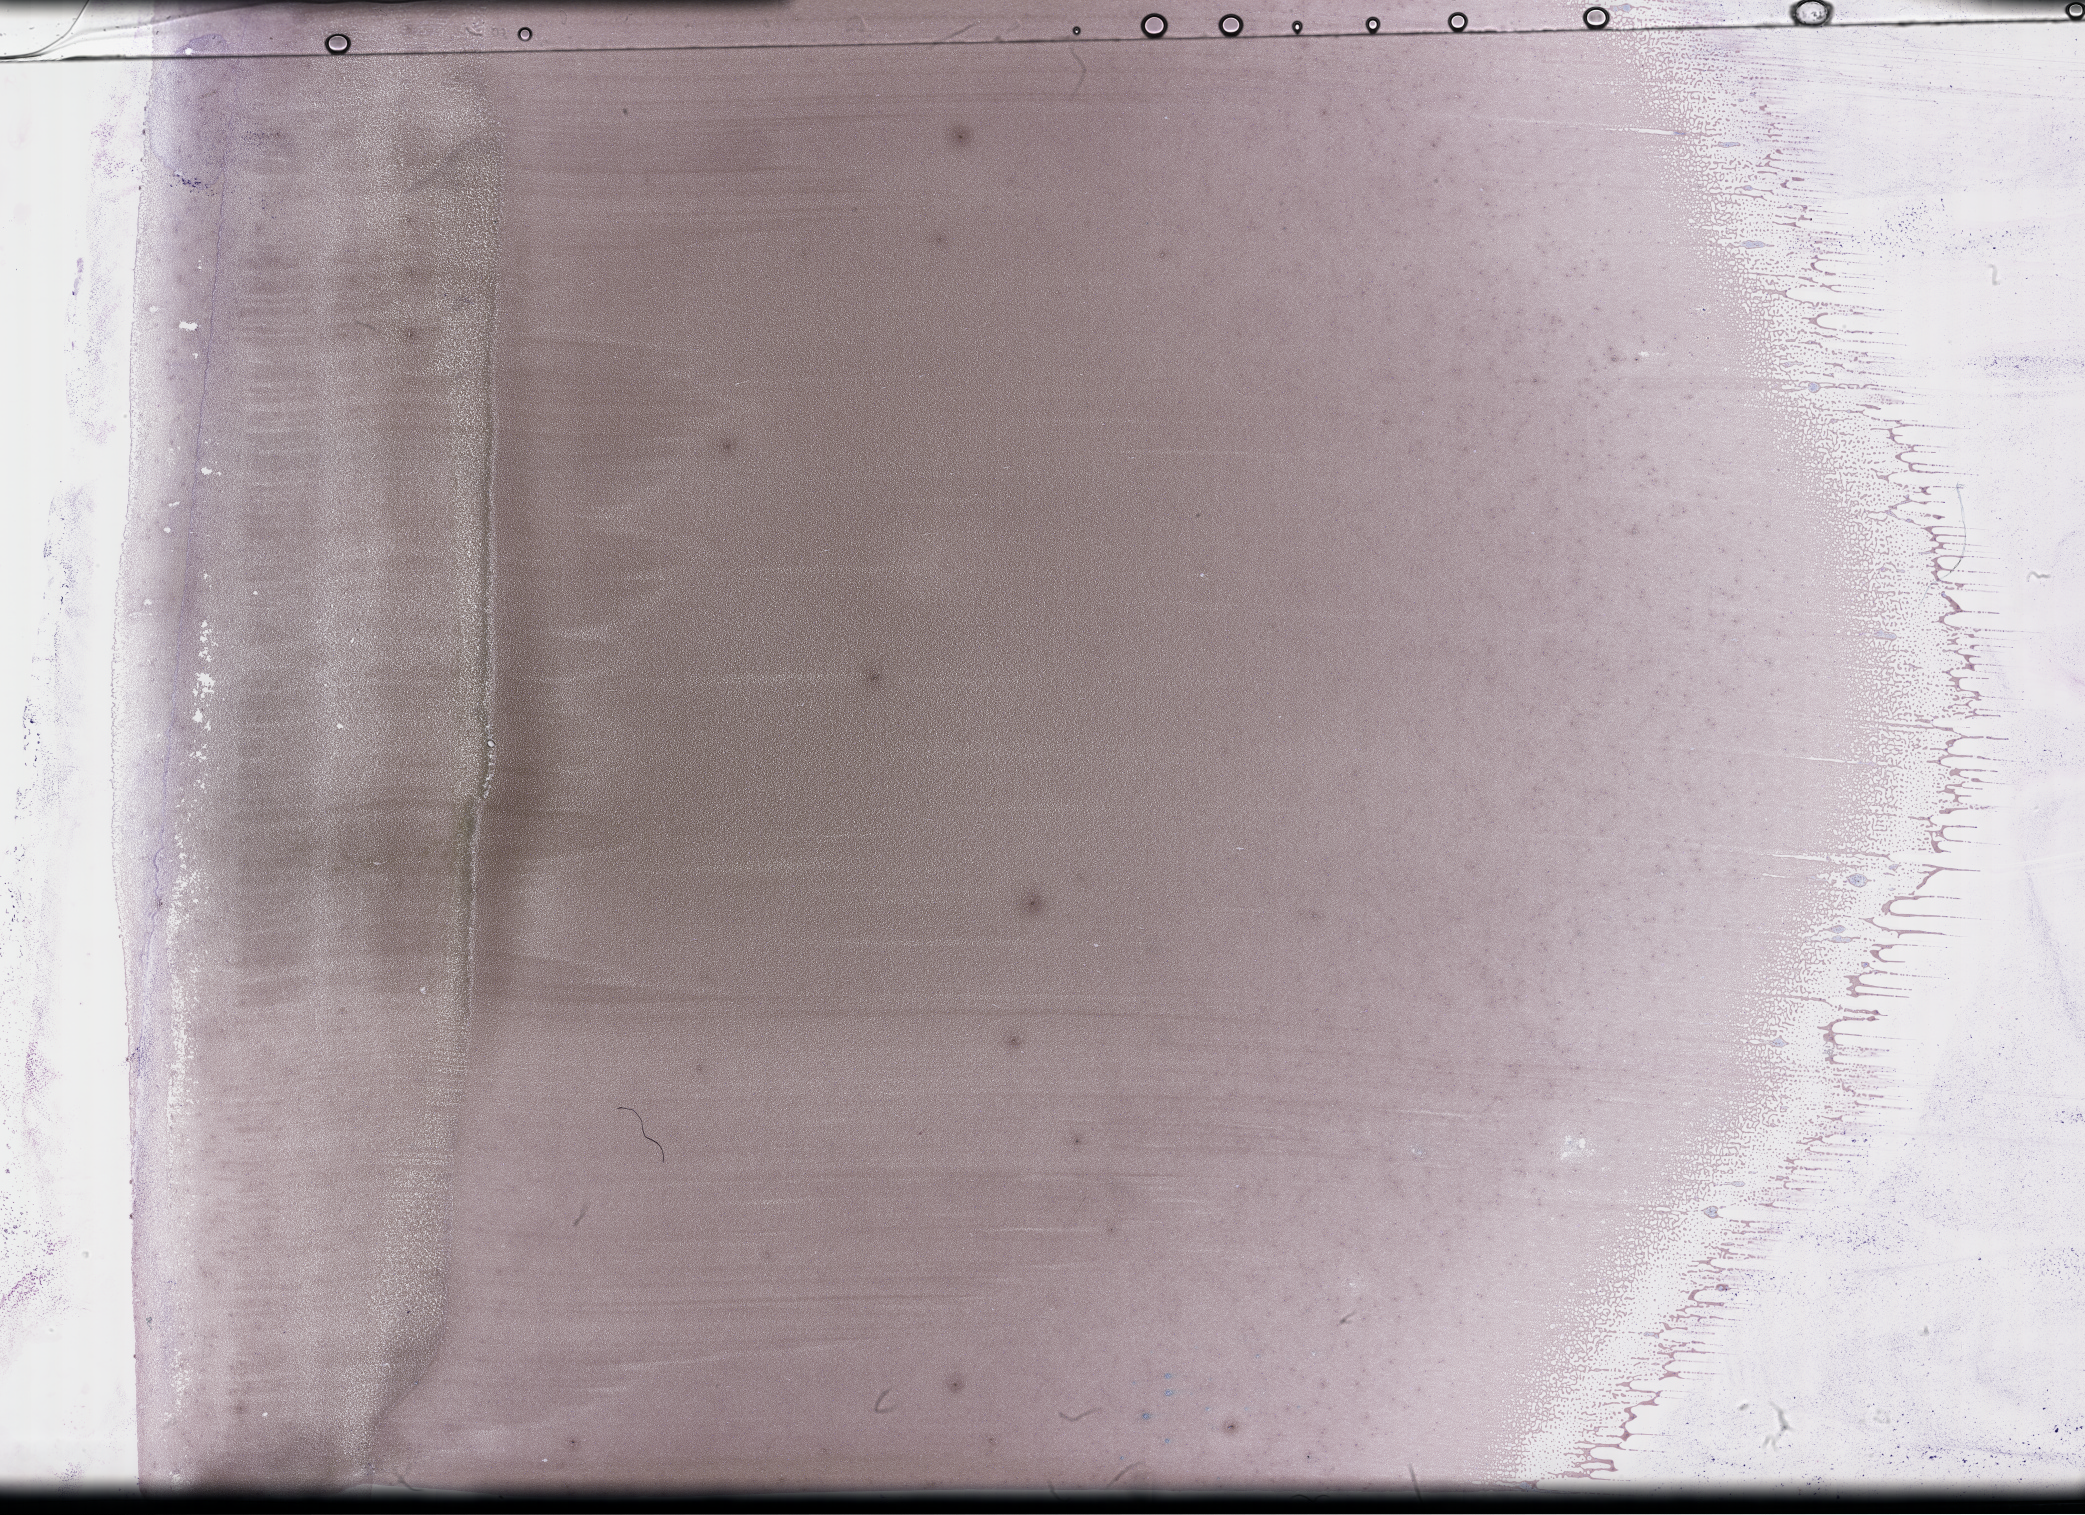
Whole-slide image of a whole blood smear, Wright–Giemsa stain — whole scanned area (about 33.7 x 24.5 mm) shown as a low-resolution overview, EDTA-anticoagulated smear. Patient: female.
Patient diagnosis: Plasma Cell Myeloma.